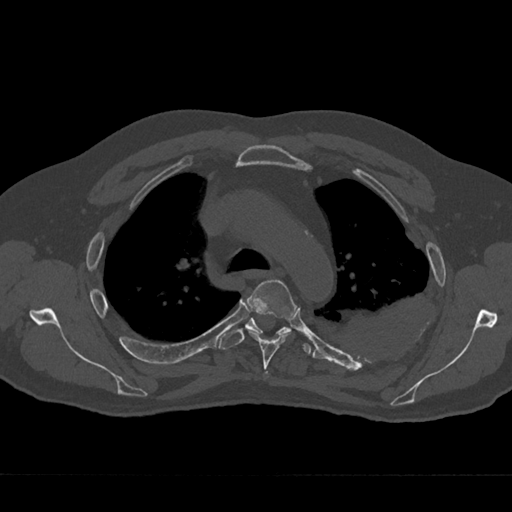
CT including the spine, one axial slice; slice 503 of 797 in the series (ordered by position); 120 kVp; bone window (W 1800 / L 400 HU); 0.5 mm slice thickness; 512 × 512 image matrix. Patient: male, 75 years. From the clinical record (not read from this slice): primary cancer: renal.
Structures marked on this image (semi-automatically segmented with operator editing):
- T4 vertebra: bounding box <245,279,295,376> (left, top, right, bottom; pixels)
- T5 vertebra: <219,318,311,354>